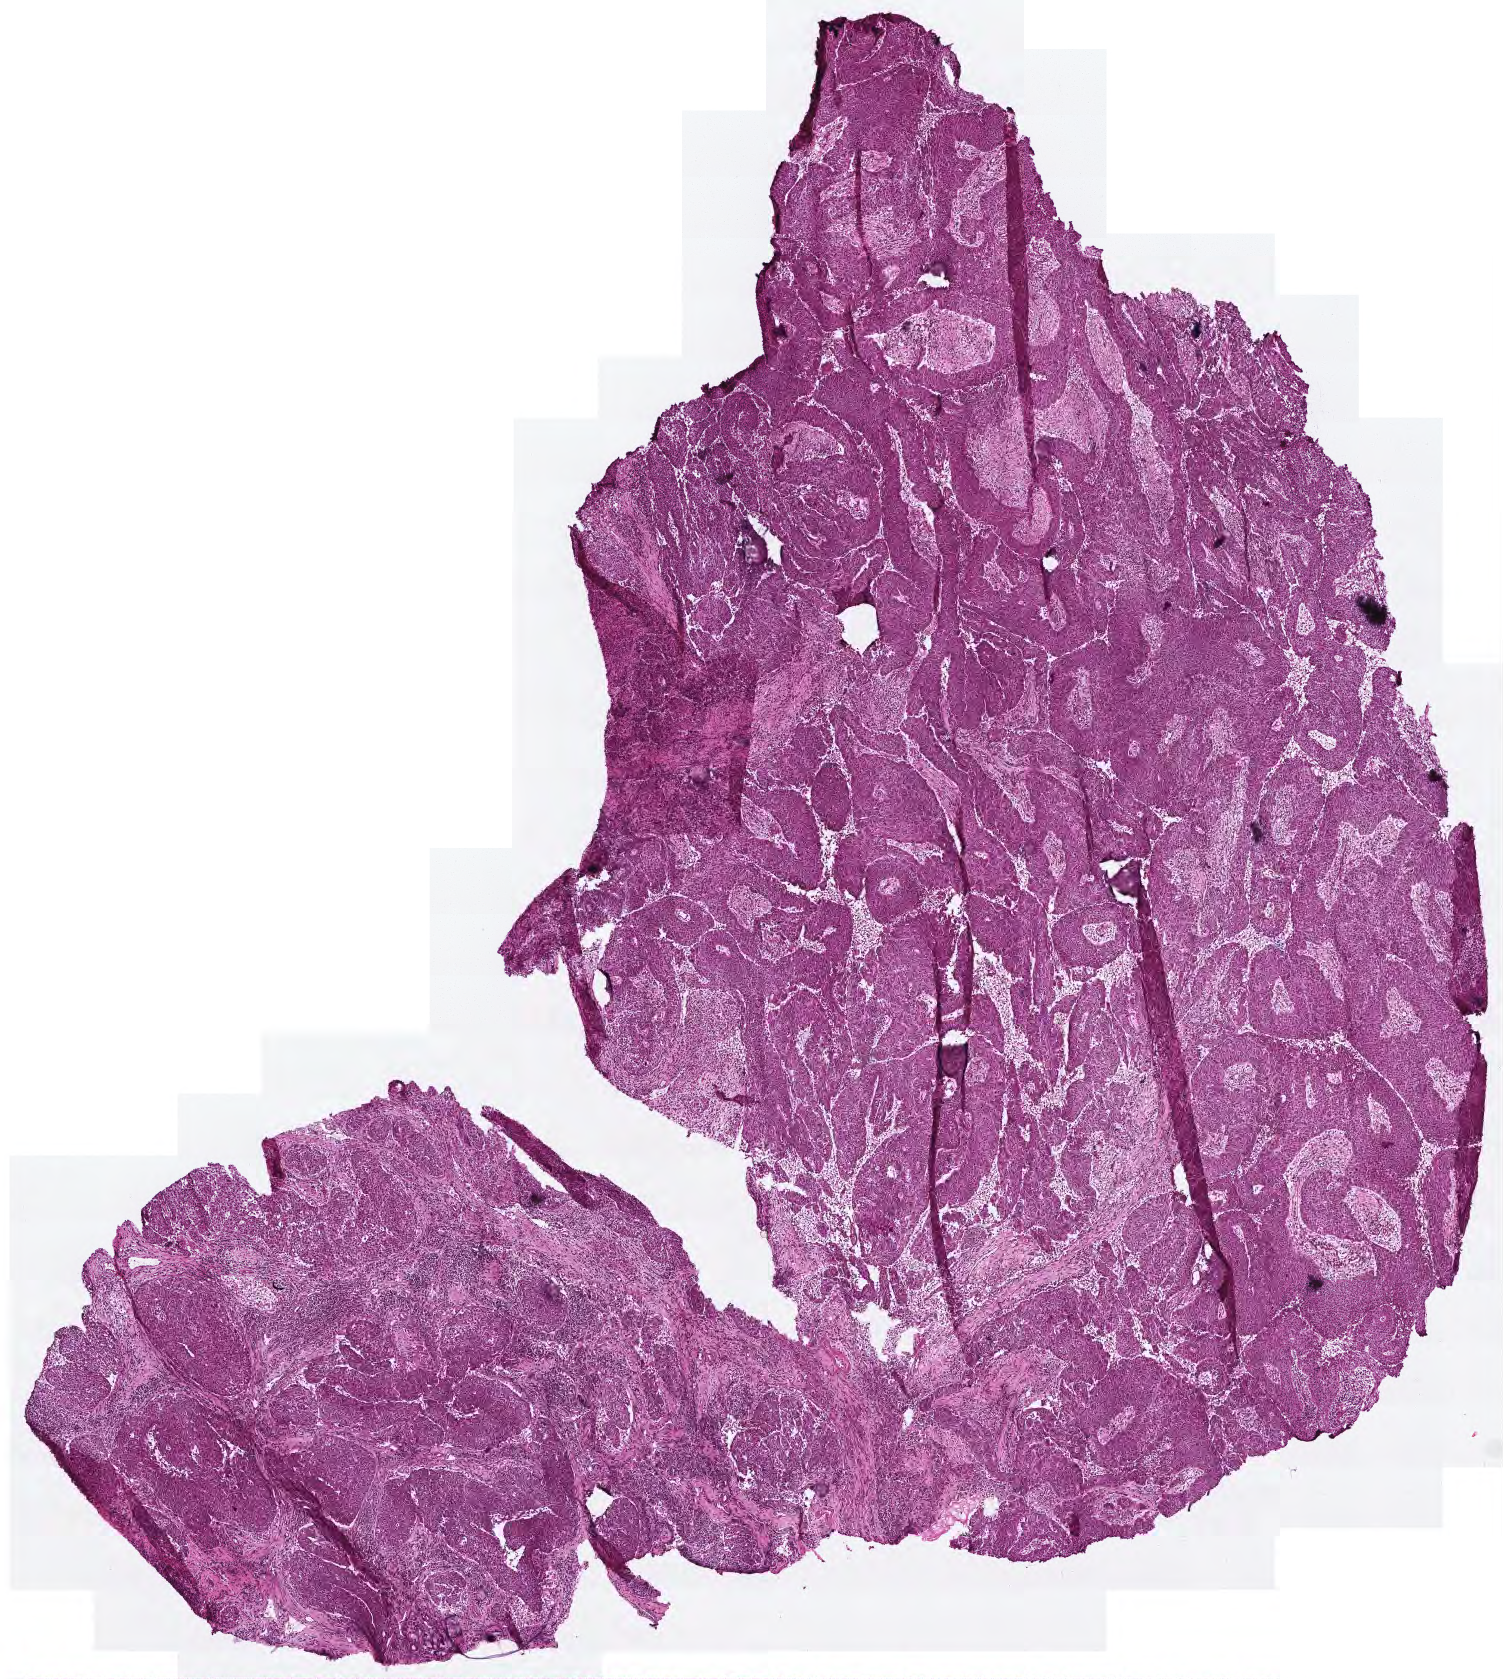
H&E-stained whole-slide image, whole scanned area (about 3.0 x 3.4 mm) shown as a low-resolution overview. Frozen section from the top of the tissue portion. Sample: primary tumour, head and neck. Male, age 58 years at initial diagnosis. Pathologist review of this section (percent, as recorded): tumour cells 80%, tumour nuclei 85%.
Pathologic diagnosis: Squamous cell carcinoma, NOS (overlapping lesion of lip, oral cavity and pharynx).